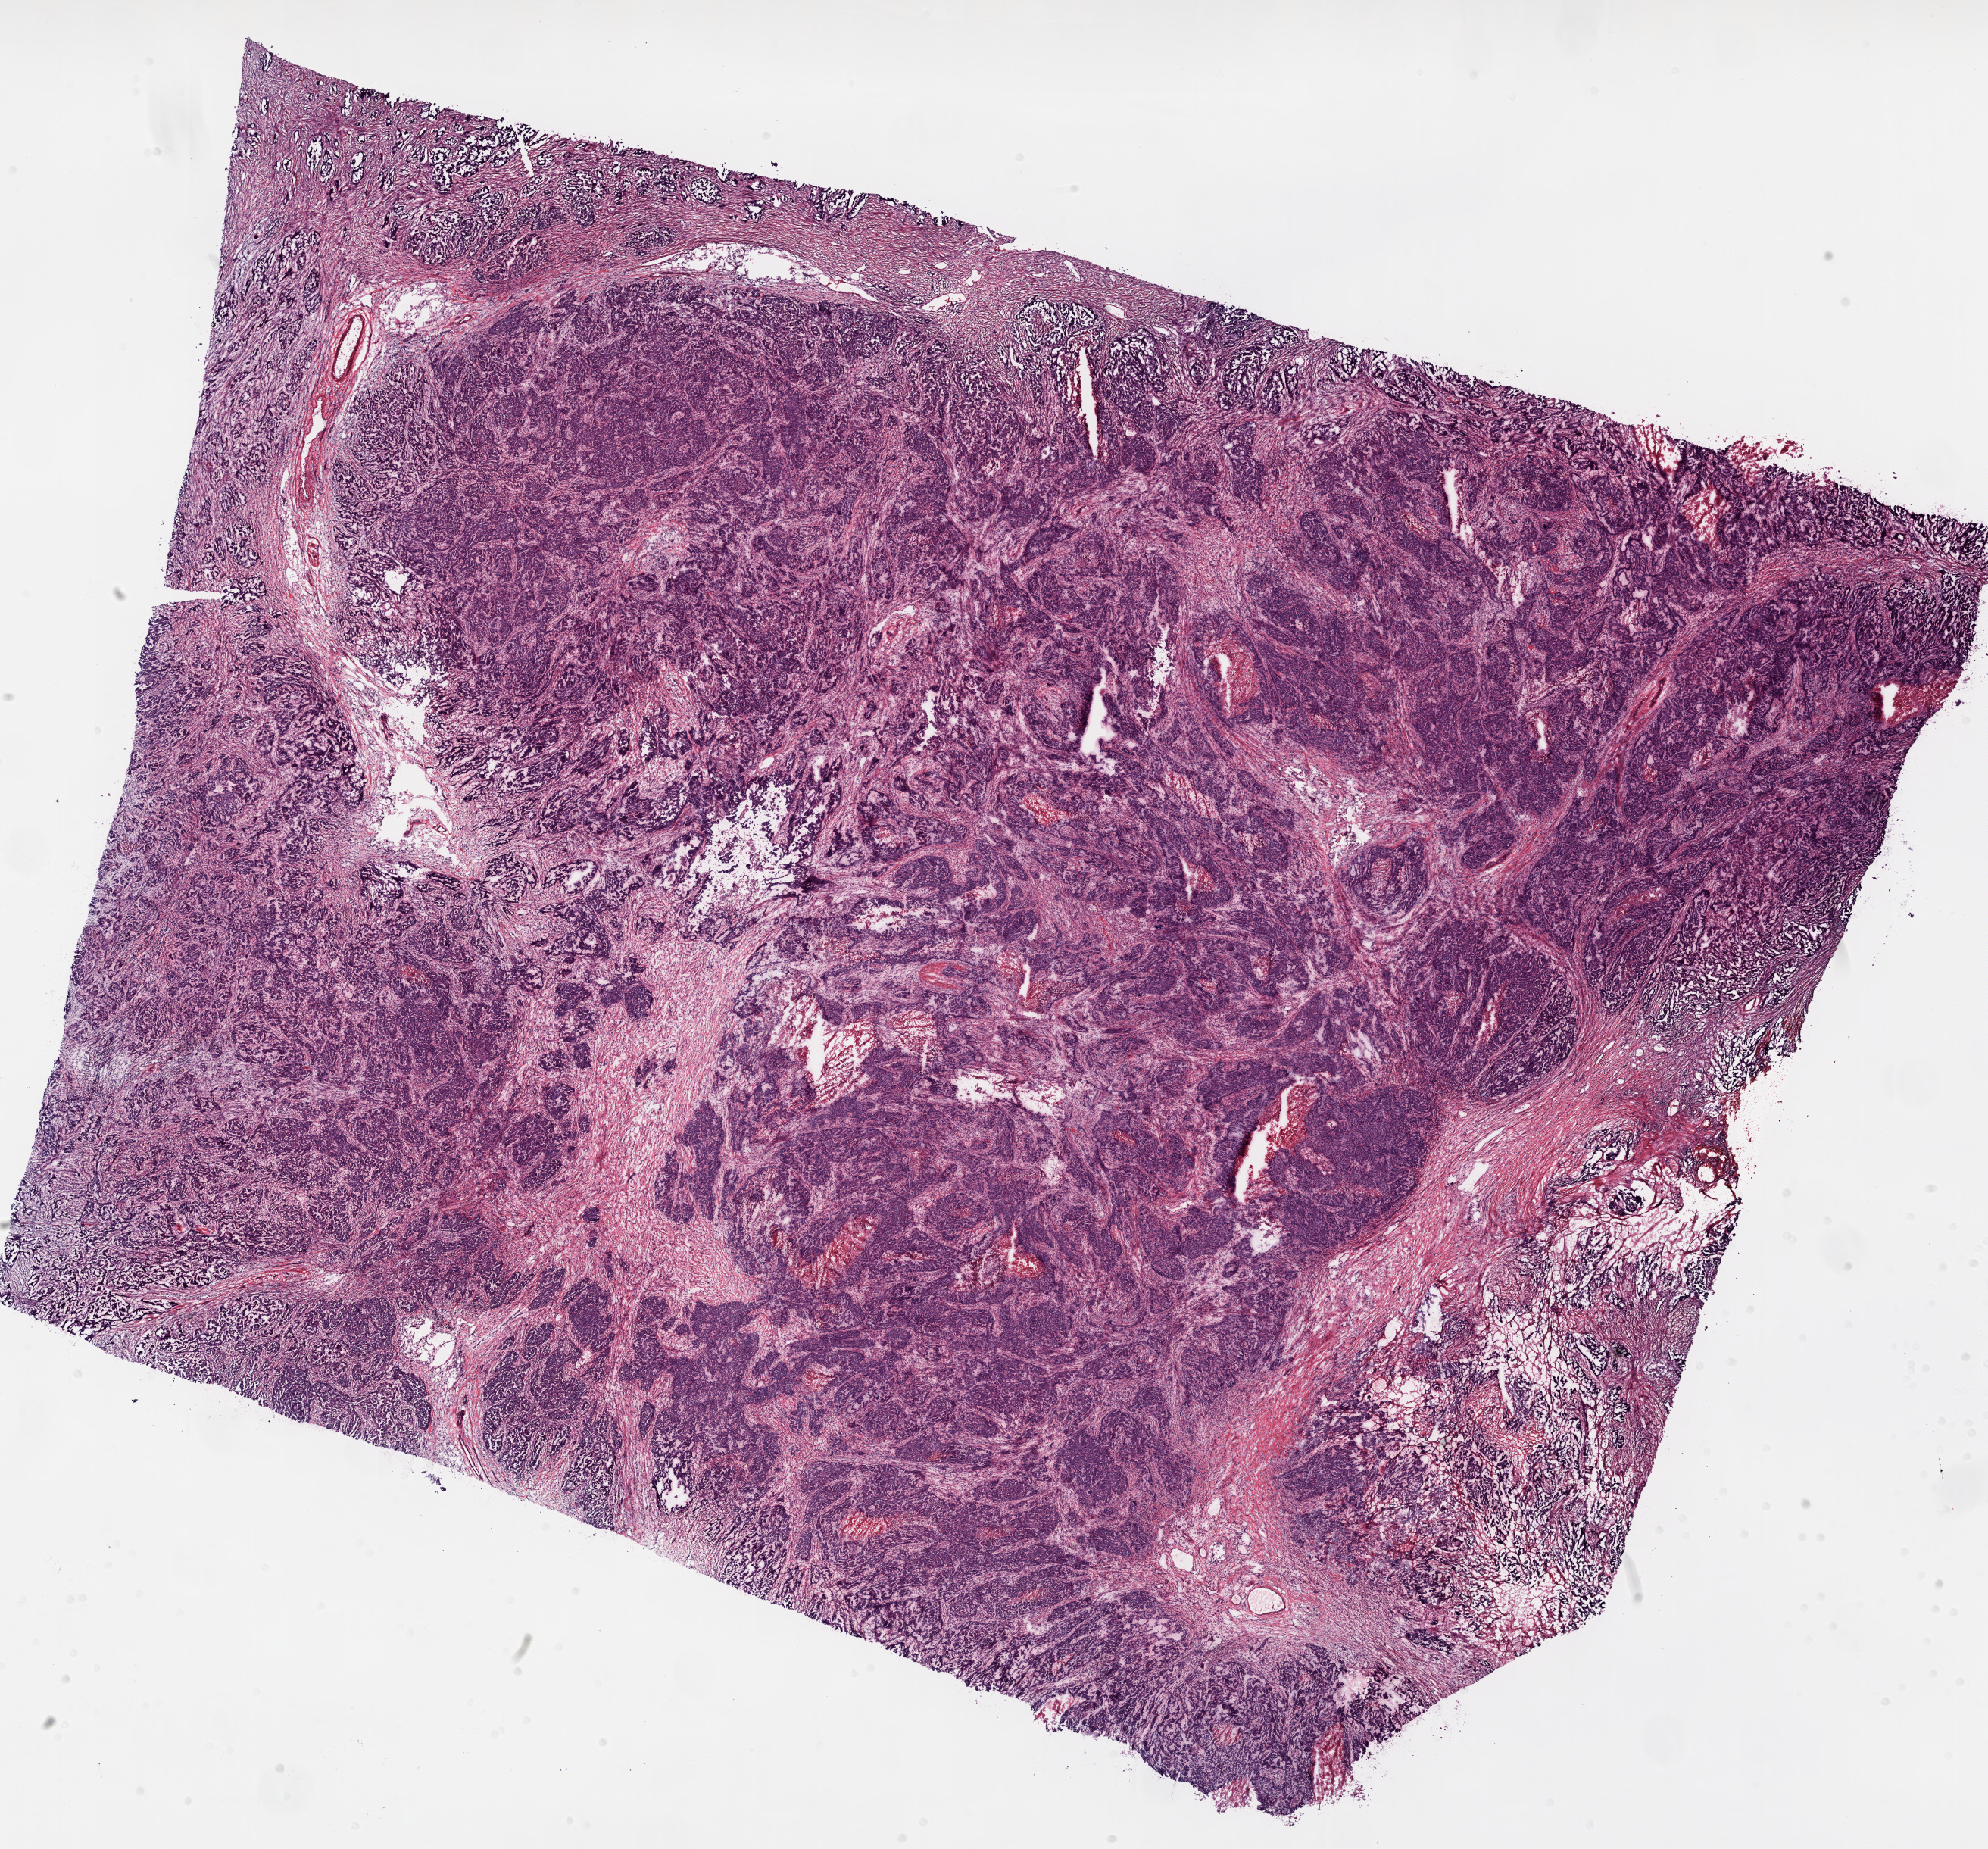
Whole-slide histology image, H&E, whole scanned area (about 21.1 x 19.6 mm, from a 20x scan) shown as a low-resolution overview. Frozen section from the top of the tissue portion. Sample: primary tumour, ovary. Patient: female, age at initial diagnosis 64 years. Histologic grade: G3 (poorly differentiated). Pathologist review of this section (percent, as recorded): tumour cells 85%, tumour nuclei 90%, normal cells 0%, stromal cells 10%, necrosis 5%.
FIGO stage: IV. Diagnosis: Serous cystadenocarcinoma, NOS.